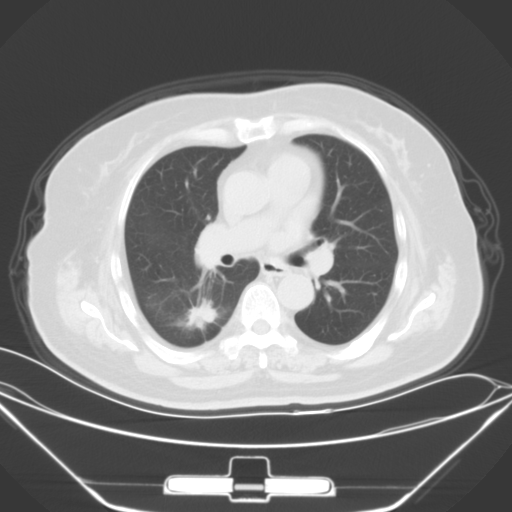
Chest CT, one axial slice. Slice 36 of 64 in the series (ordered by position). Lung window (W 1500 / L -600 HU). 5 mm slice thickness. 512 × 512 image matrix, field of view 396 × 396 mm. Patient: female, 70 years. Case-level facts recorded for this patient, not image findings: clinical TNM (as recorded): T2 N0 M3.
Structures marked on this image (bounding box drawn by a radiologist):
- lung tumour (recorded histology: adenocarcinoma): bounding box [x1, y1, x2, y2] px = [163, 295, 226, 340]